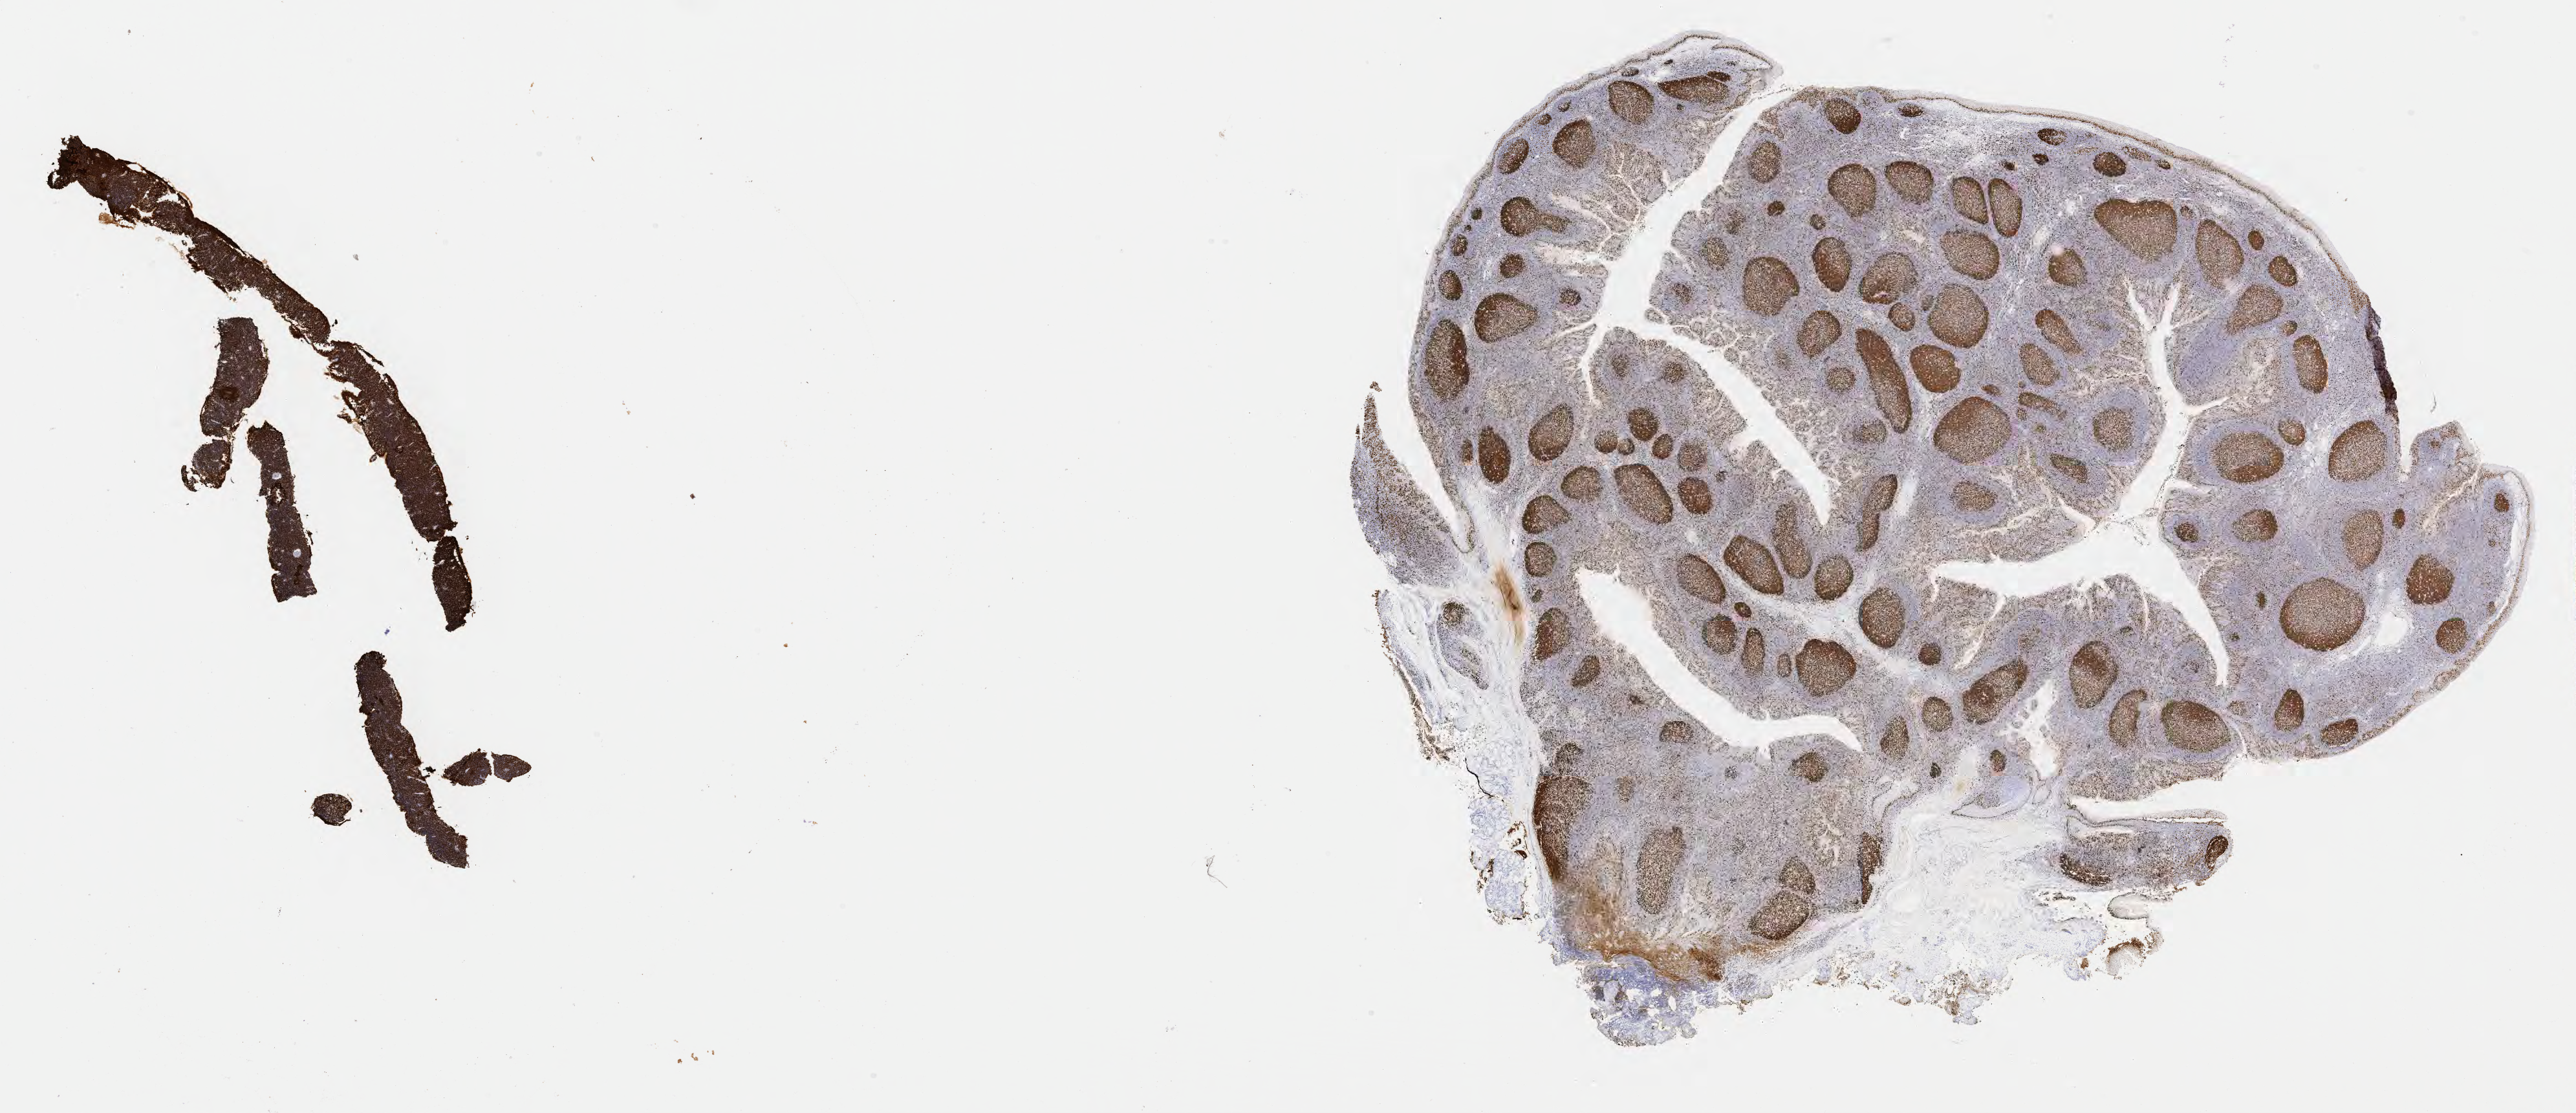
Whole-slide image, immunohistochemical stain for Ki-67 — shown as a low-resolution overview of the whole scanned area (about 32.2 x 13.9 mm); tumor tissue. Male, age 8 years at initial diagnosis.
Diagnosis: Burkitt lymphoma, NOS.